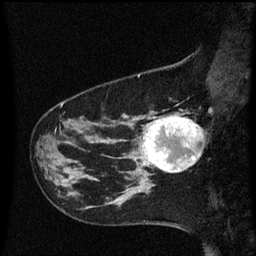
Breast MRI (dynamic contrast-enhanced), one sagittal slice. Slice 18 of 60 in the series (ordered by position). Dynamic contrast-enhanced series, image 2 of 3 at this slice position (ordered by acquisition). 1.5 T. TE 4.2 ms, TR 8.4 ms. 256 × 256 image matrix, field of view 200 × 200 mm. Patient: female, 41 years. From the clinical record (not read from this slice): setting: breast cancer imaged before/during neoadjuvant chemotherapy; receptor status: triple-negative.
Annotated regions visible in this slice (semi-automatic segmentation, software-assisted and operator-edited):
- analysis volume of interest (the breast-tissue region the enhancement analysis was run in; not a lesion): bounding box [x1, y1, x2, y2] px = [138, 112, 202, 177]
- tumour enhancement mask (voxels above the 70 % enhancement threshold inside the analysis volume of interest): [143, 116, 200, 173]